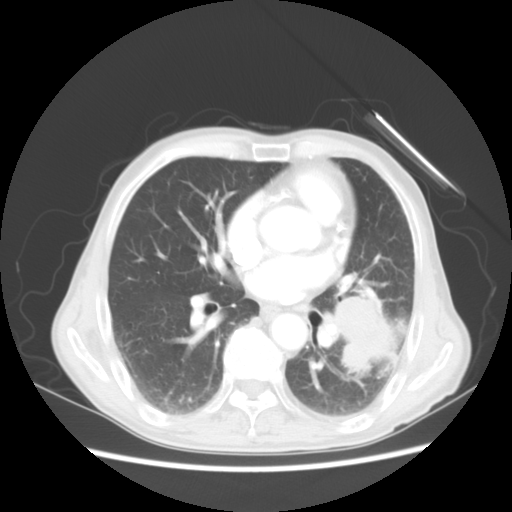
Chest CT, one axial slice. Slice 24 of 51 in the series (ordered by position). Reconstruction kernel STANDARD. Lung window (W 1500 / L -600 HU). 5 mm slice thickness. 512 × 512 image matrix, field of view 360 × 360 mm. Patient: male, 64 years. From the clinical record (not read from this slice): clinical TNM (as recorded): T4 N0 M0.
Annotated regions visible in this slice (bounding box drawn by a radiologist):
- lung tumour (recorded histology: squamous cell carcinoma): bounding box <323,280,407,386> (left, top, right, bottom; pixels)